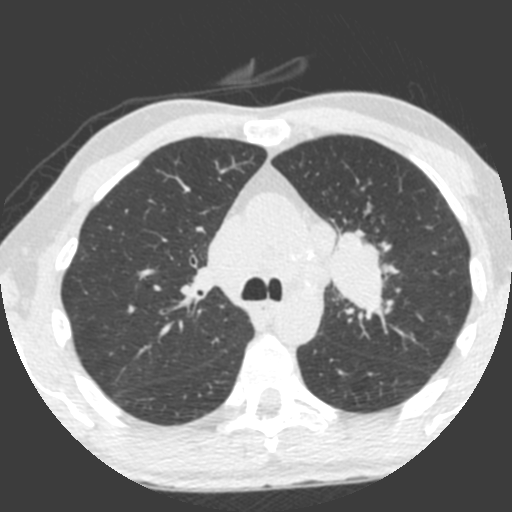
Low-dose screening chest CT, axial slice; third screening round (two years after baseline); lung window (W 1500 / L -600 HU); 2 mm slice thickness; standard (soft-tissue) reconstruction kernel (B); slice 148 of 212 in the series; 512 × 512 image matrix, field of view 315 × 315 mm. Male participant, aged 55 years at enrolment. Current smoker at enrolment.
Lesion marked by an expert reader, box from (x=308, y=229) to (x=391, y=323) px. The exam's reader record, not a measurement of the box and not confirmed to be the same lesion: non-calcified nodule or mass ≥4 mm, left upper lobe, 49 × 29 mm, spiculated (stellate) margins, soft tissue attenuation, pre-existing on the prior screen: yes; interval growth: yes. Later outcome: lung cancer diagnosed 0 days after this screen — small cell carcinoma, NOS, left upper lobe, undifferentiated (G4), stage IV (AJCC 6th edition), 60 mm at pathology.